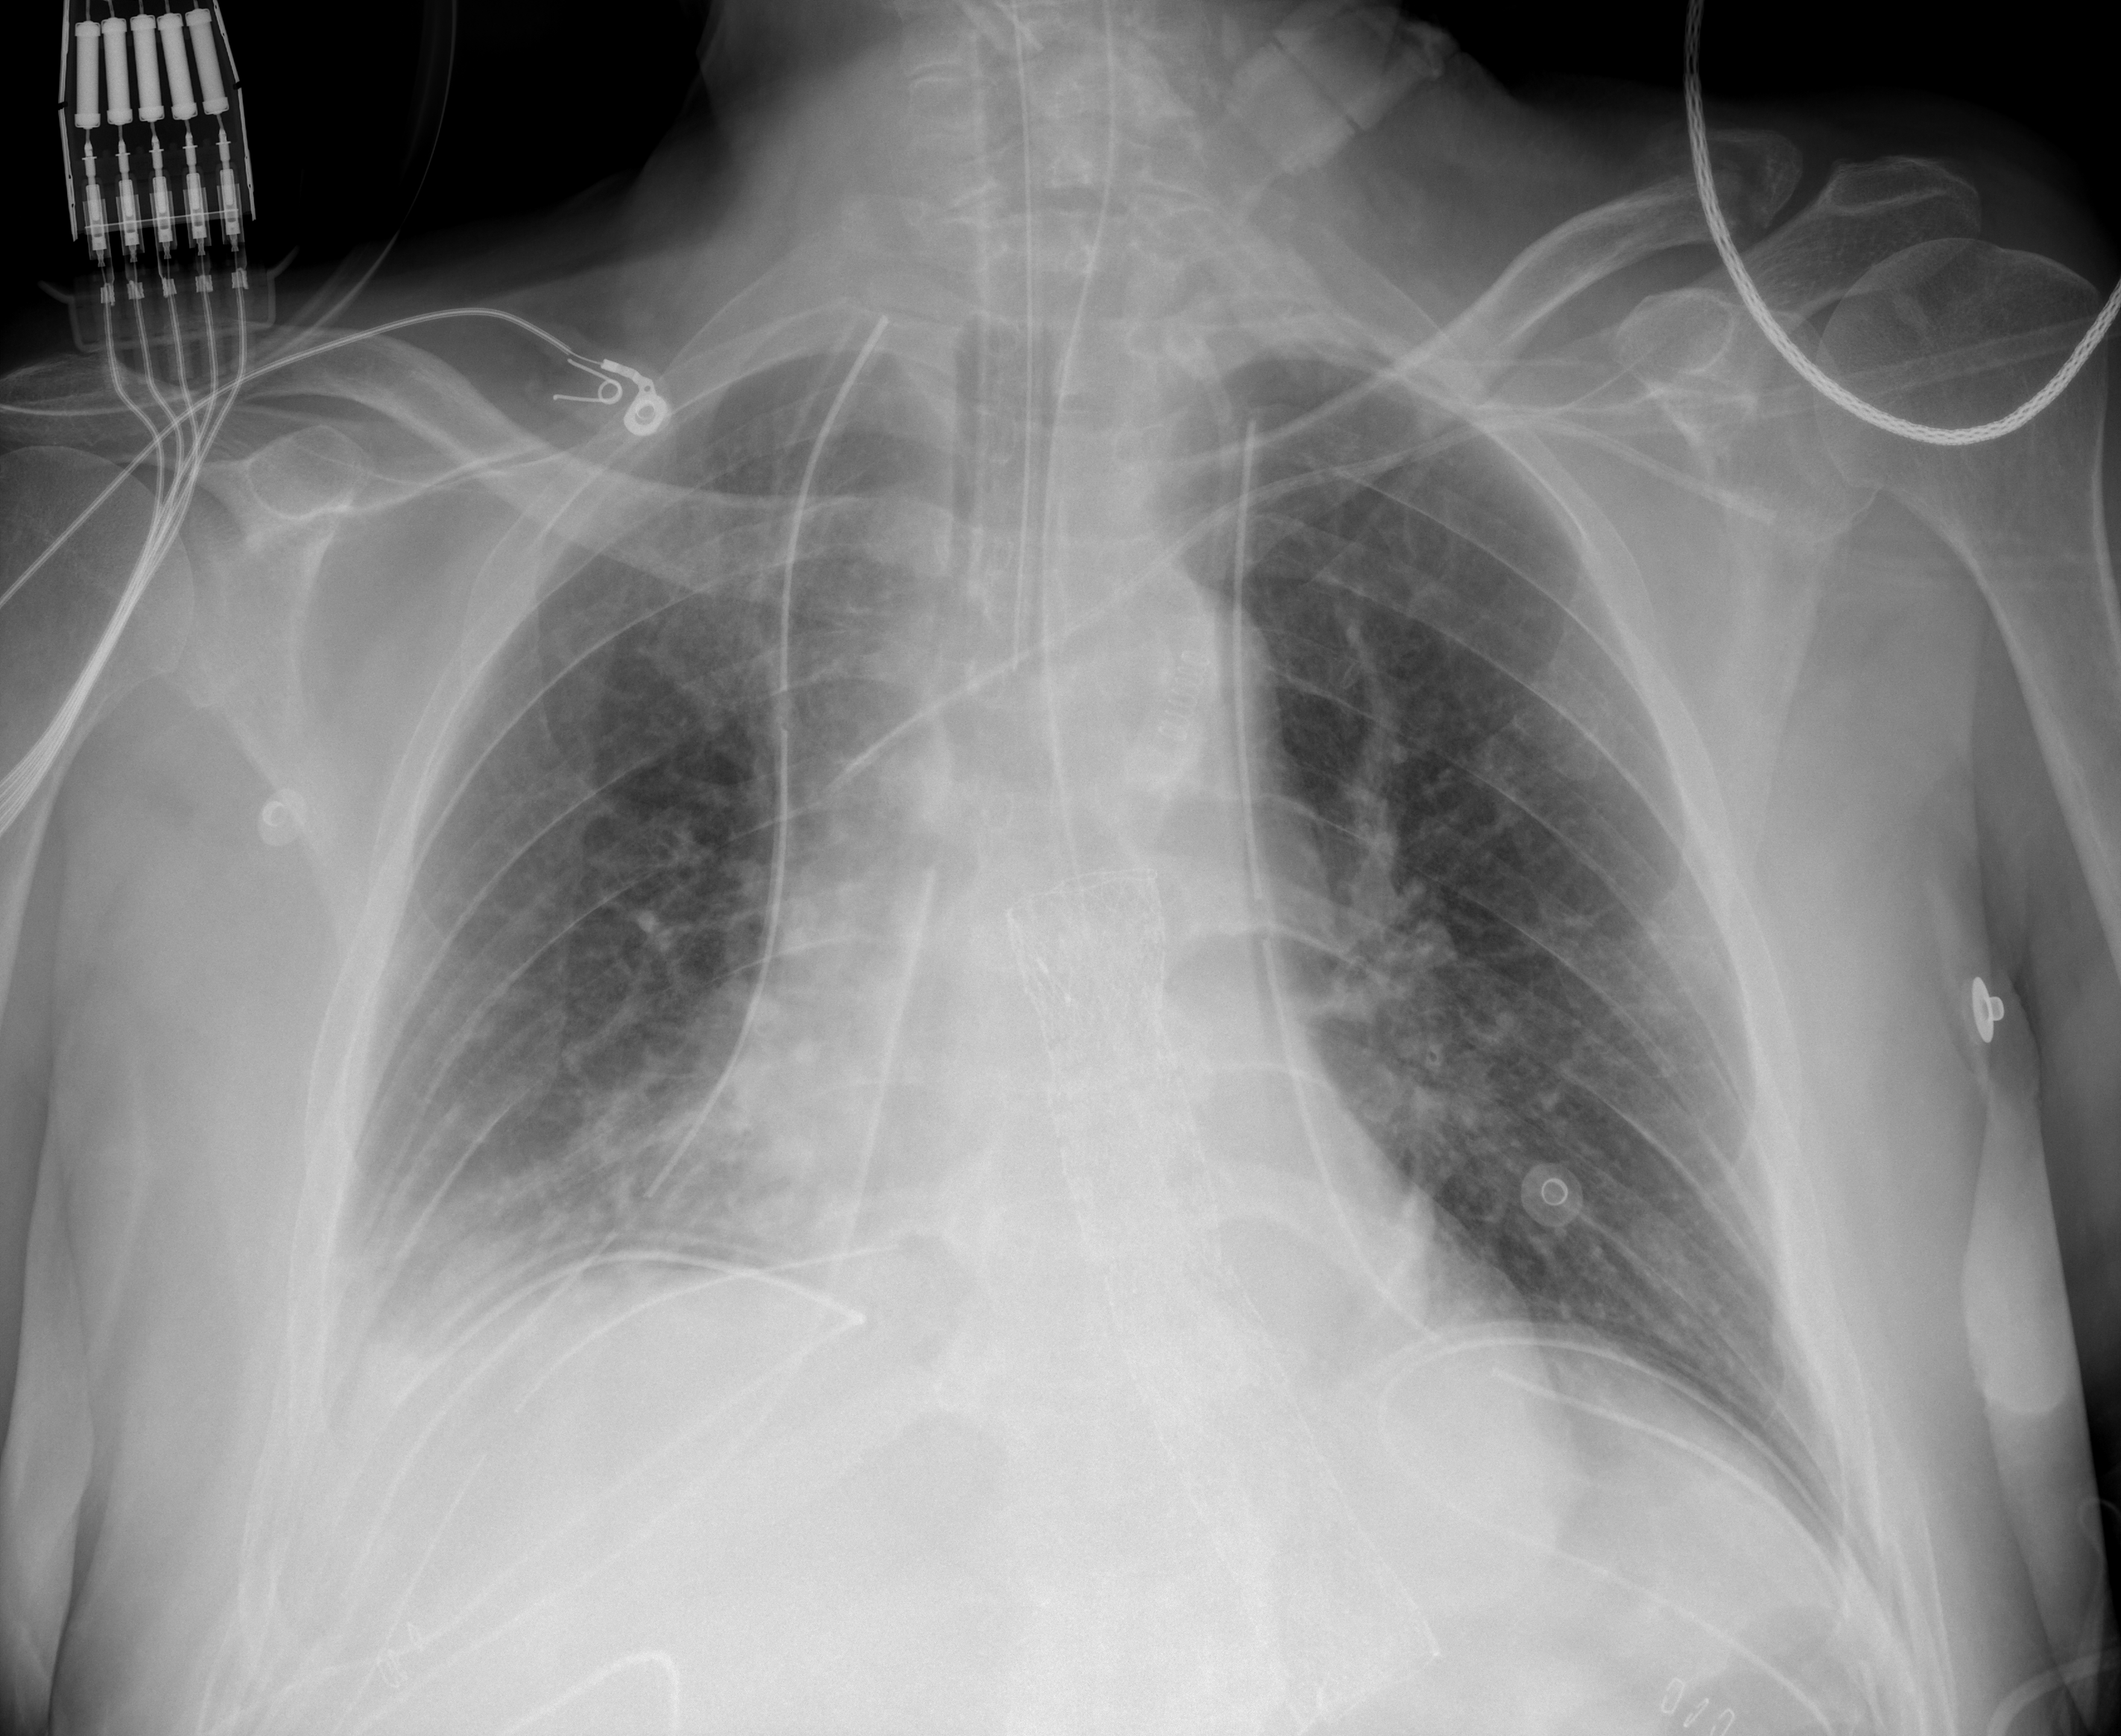
Chest X-ray (portable), AP projection. Male patient, age 64 years; COVID-19 (test-positive).
Key findings recorded by the radiologist: minimal right sided effusion and right basilar atelectasis.